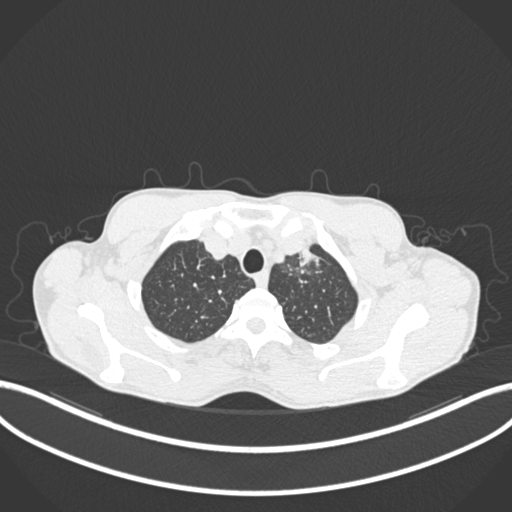
Chest CT, one axial slice. Position 180 of 211 along the scan axis. 120 kVp. Lung window (W 1500 / L -600 HU). 512 × 512 image matrix, field of view 400 × 400 mm. Male patient, age 58 years. From the clinical record (not read from this slice): clinical TNM (as recorded): T1c N1 M0.
Structures marked on this image (rectangle marked by the reading radiologist):
- lung tumour (recorded histology: adenocarcinoma): box from (x=295, y=241) to (x=324, y=276) px